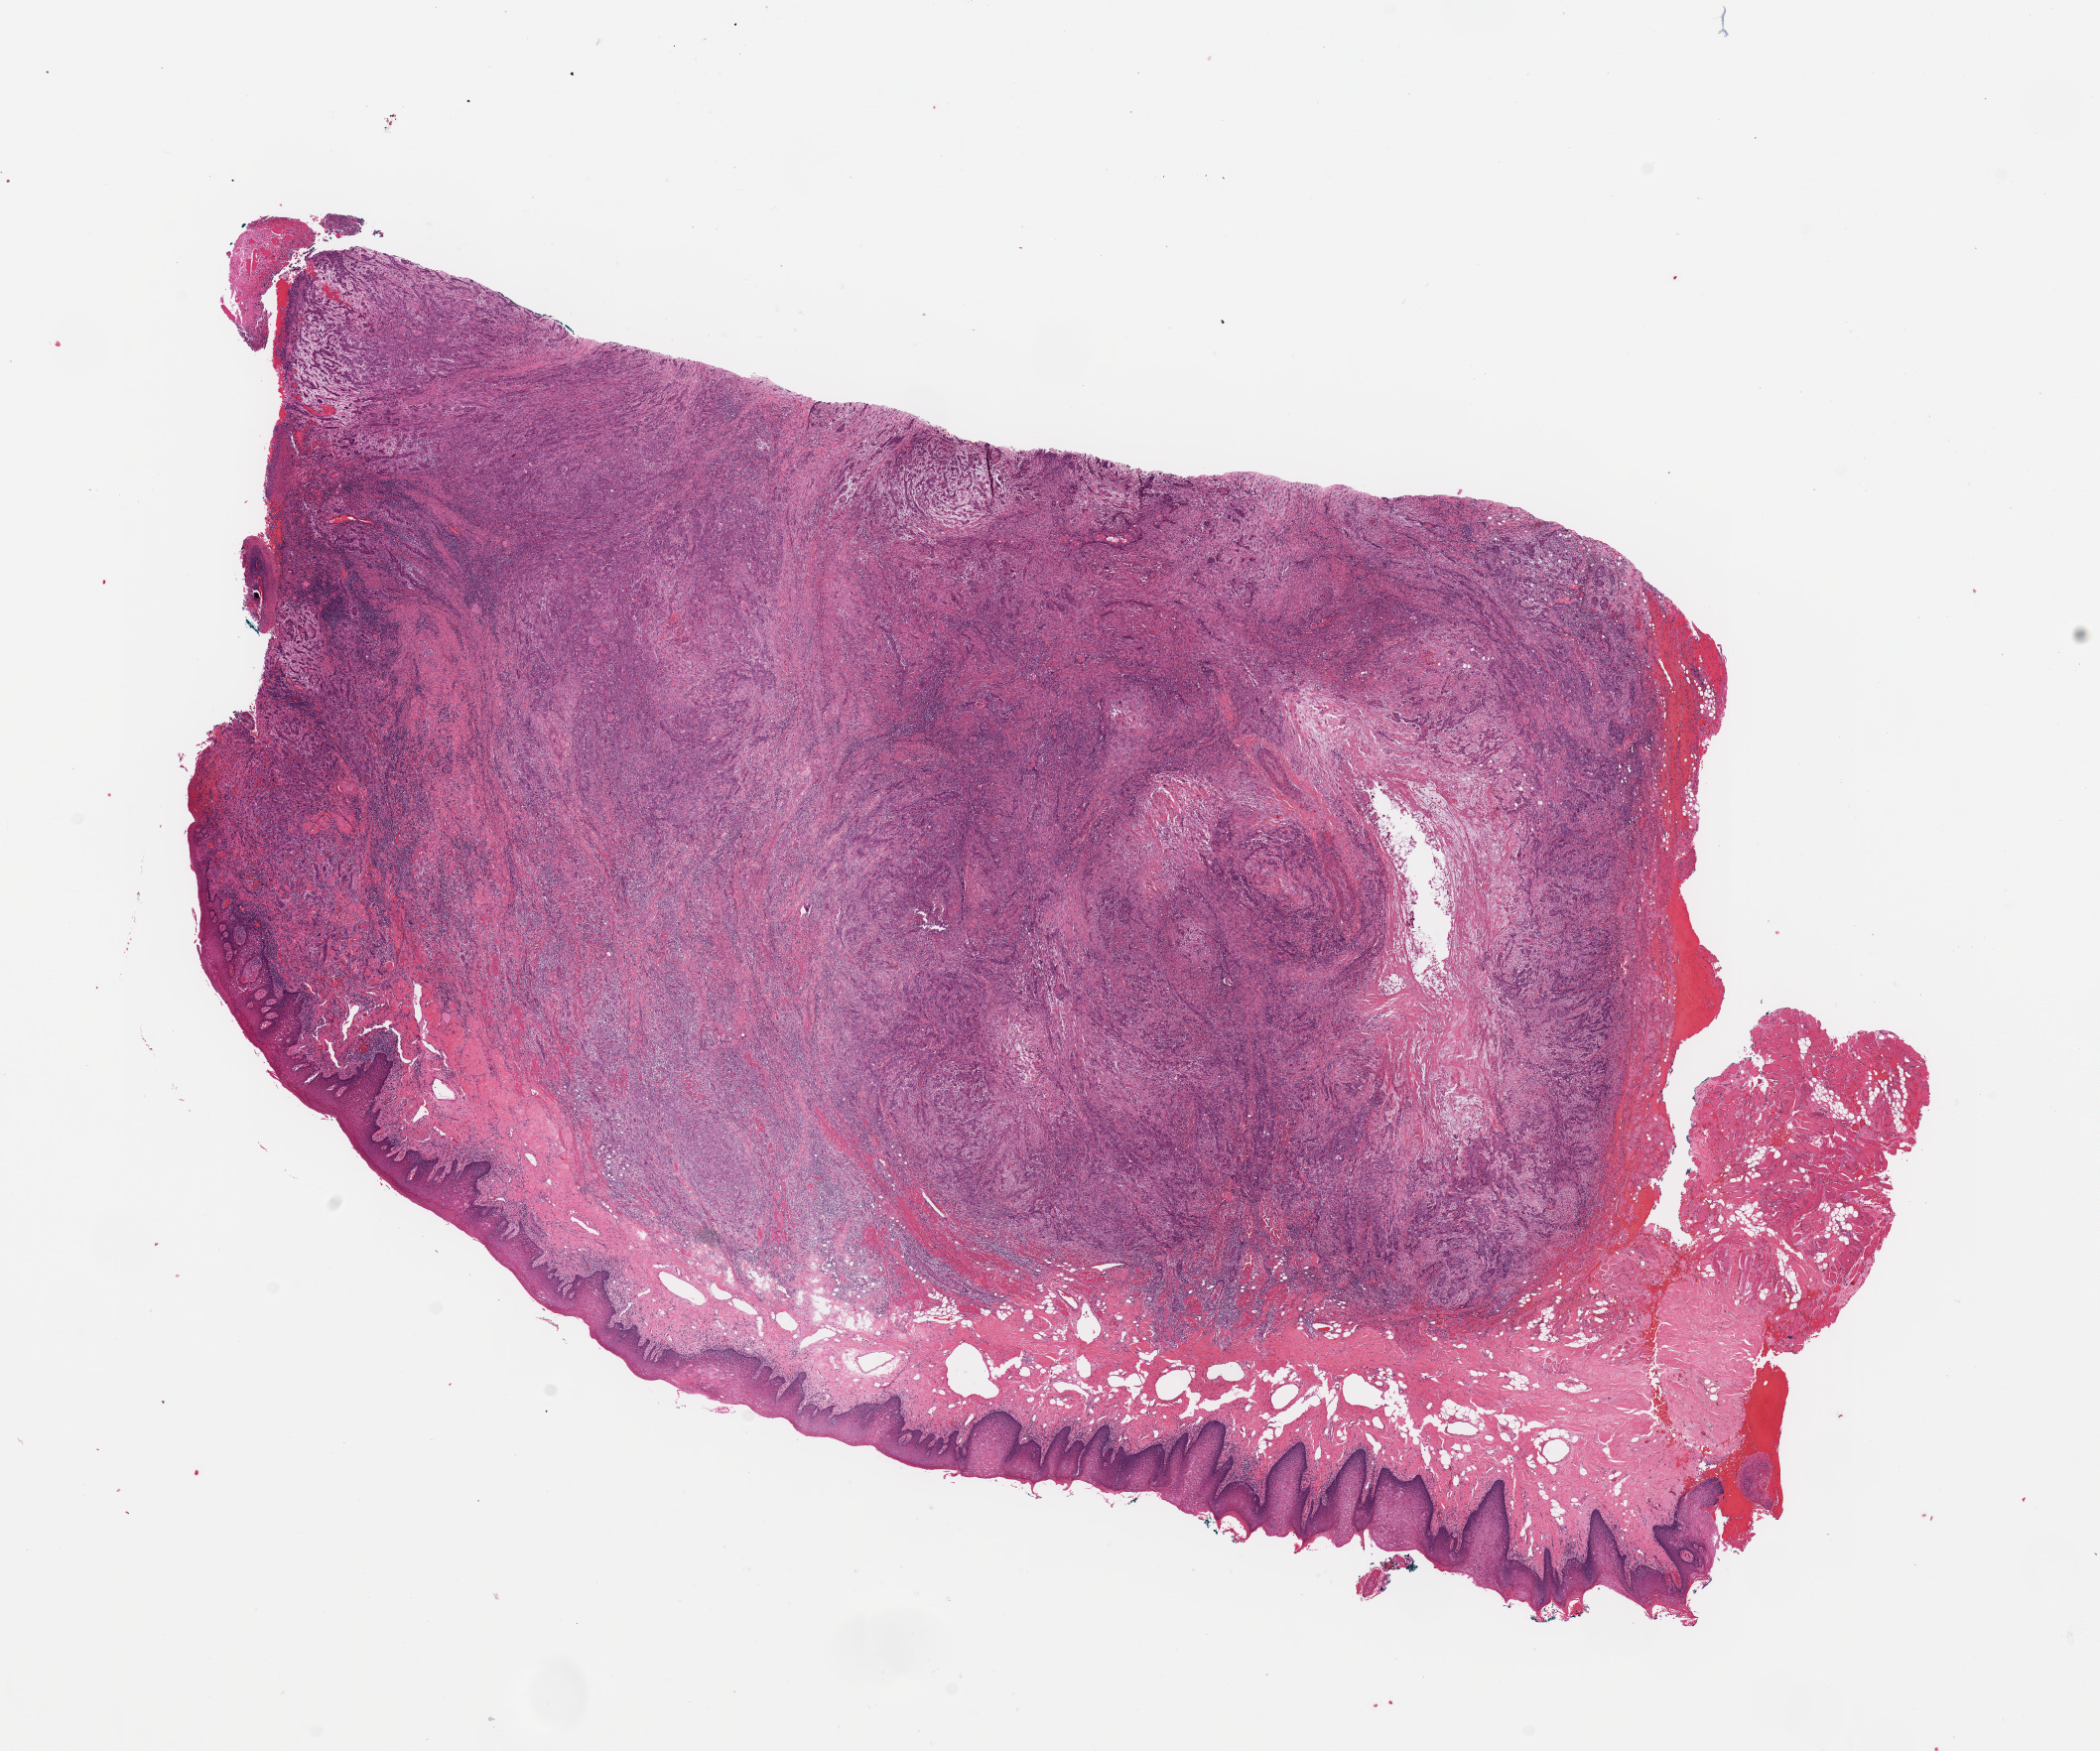
Digitized H&E-stained tissue section (whole slide), a low-resolution overview of the entire scanned area, about 16.7 x 14.0 mm; head and neck, tissue type not recorded. Male, 50 y/o.
- patient diagnosis: Squamous cell carcinoma, NOS (tongue, NOS)